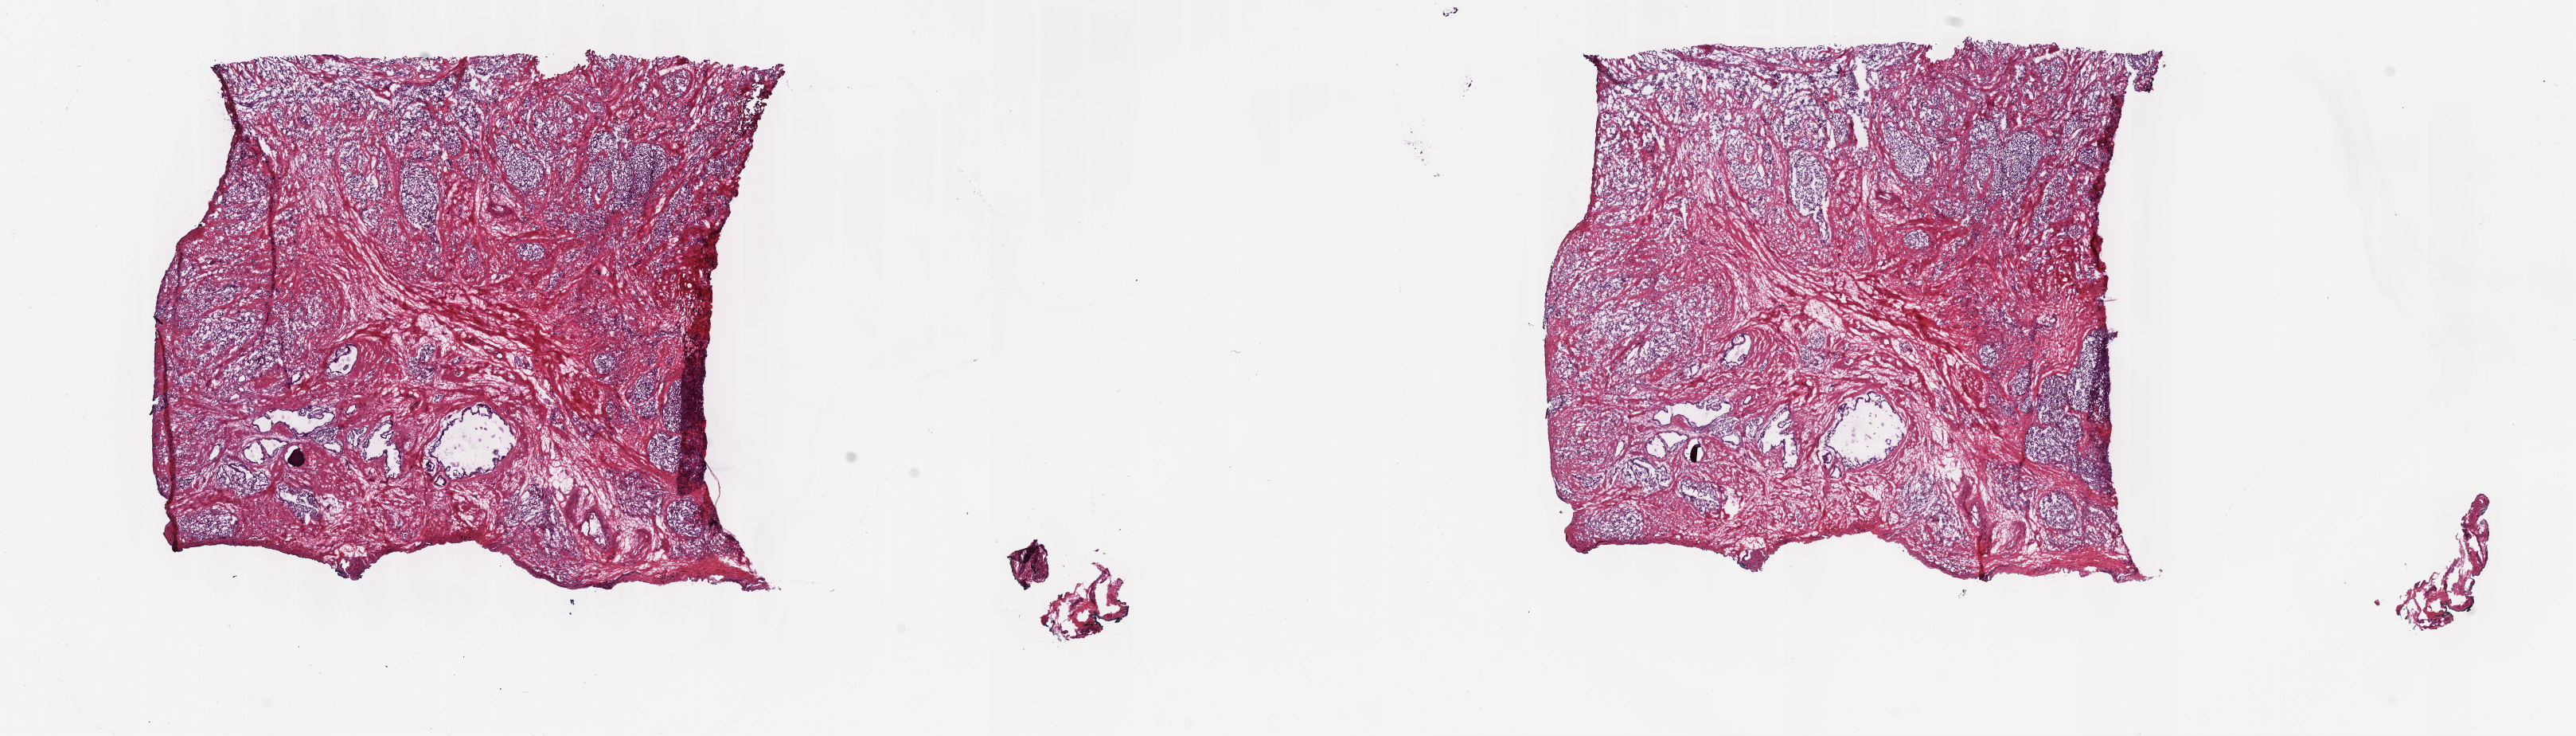
Digitized Hematoxylin and eosin (H&E) stained tissue section (whole slide) — low-resolution overview of the scanned area, about 26.2 x 7.5 mm. Frozen section from the top of the tissue portion. Primary tumour sample from the prostate. Male, age 67 years at initial diagnosis. Gleason score: 9 (5+4). Composition of this section per pathologist review: tumour cells 60%, tumour nuclei 80%, normal cells 10%, stromal cells 30%, necrosis 0%. Infiltration values recorded for this section: lymphocyte infiltration 0%, monocyte infiltration 0%, neutrophil infiltration 0%.
Diagnosis: Adenocarcinoma, NOS (prostate gland).